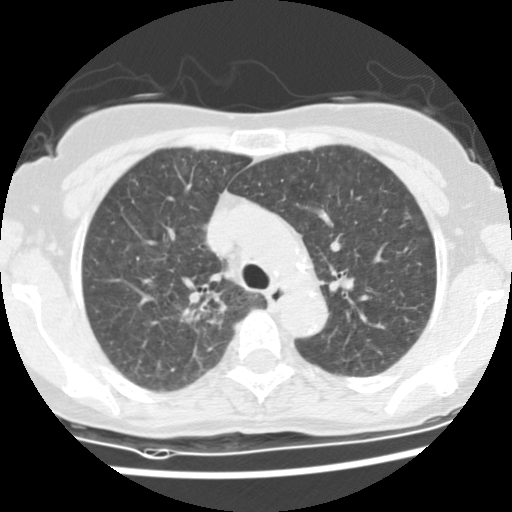
Low-dose screening chest CT, one axial slice. Reconstruction kernel STANDARD. Lung window (W 1500 / L -600 HU). 512 × 512 image matrix, field of view 298 × 298 mm.
Structures marked on this image (outlined manually by an expert reader):
- lesion 1 (tumor, upper lobe of right lung): box from (x=180, y=307) to (x=204, y=324) px